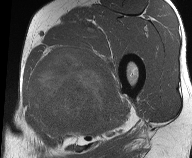
MRI of an extremity soft-tissue mass, one axial slice. Position 34 of 61 along the scan axis. MR volume resampled by the dataset authors to the PET/CT grid (not the native acquisition matrix). 3.27 mm slice thickness. 192 × 158 image matrix. Male patient. From the clinical record (not read from this slice): histological type: pleiomorphic liposarcoma; grade: high; site of the primary tumour: left thigh.
Outlined on this slice (expert contour drawn on MRI and transferred to this co-registered scan by the dataset authors):
- gross tumour volume including surrounding oedema: bounding box <27,44,117,138> (left, top, right, bottom; pixels)
- gross tumour volume (mass): <27,46,115,129>